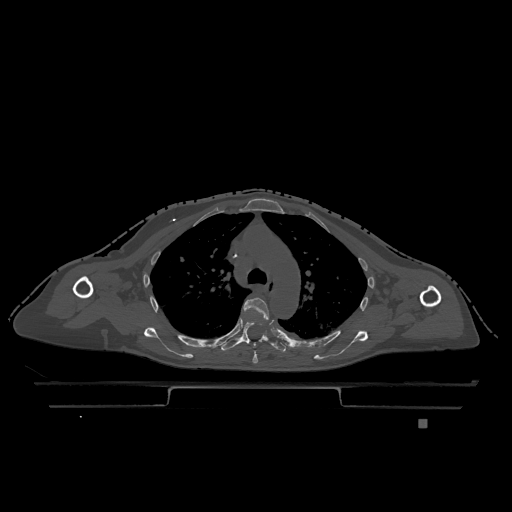
CT including the spine, one axial slice; slice 855 of 1317 in the series (ordered by position); bone window (W 1800 / L 400 HU); 0.5 mm slice thickness; 512 × 512 image matrix, field of view 500 × 500 mm. Female patient, age 74 years. From the clinical record (not read from this slice): primary cancer: lung; vertebrae with lytic lesions (as recorded): T1, T4, T5, T6, L4, L5.
Structures marked on this image (semi-automatic segmentation, software-assisted and operator-edited):
- T4 vertebra: bounding box [x1, y1, x2, y2] px = [244, 297, 270, 364]
- T5 vertebra: [221, 321, 287, 353]